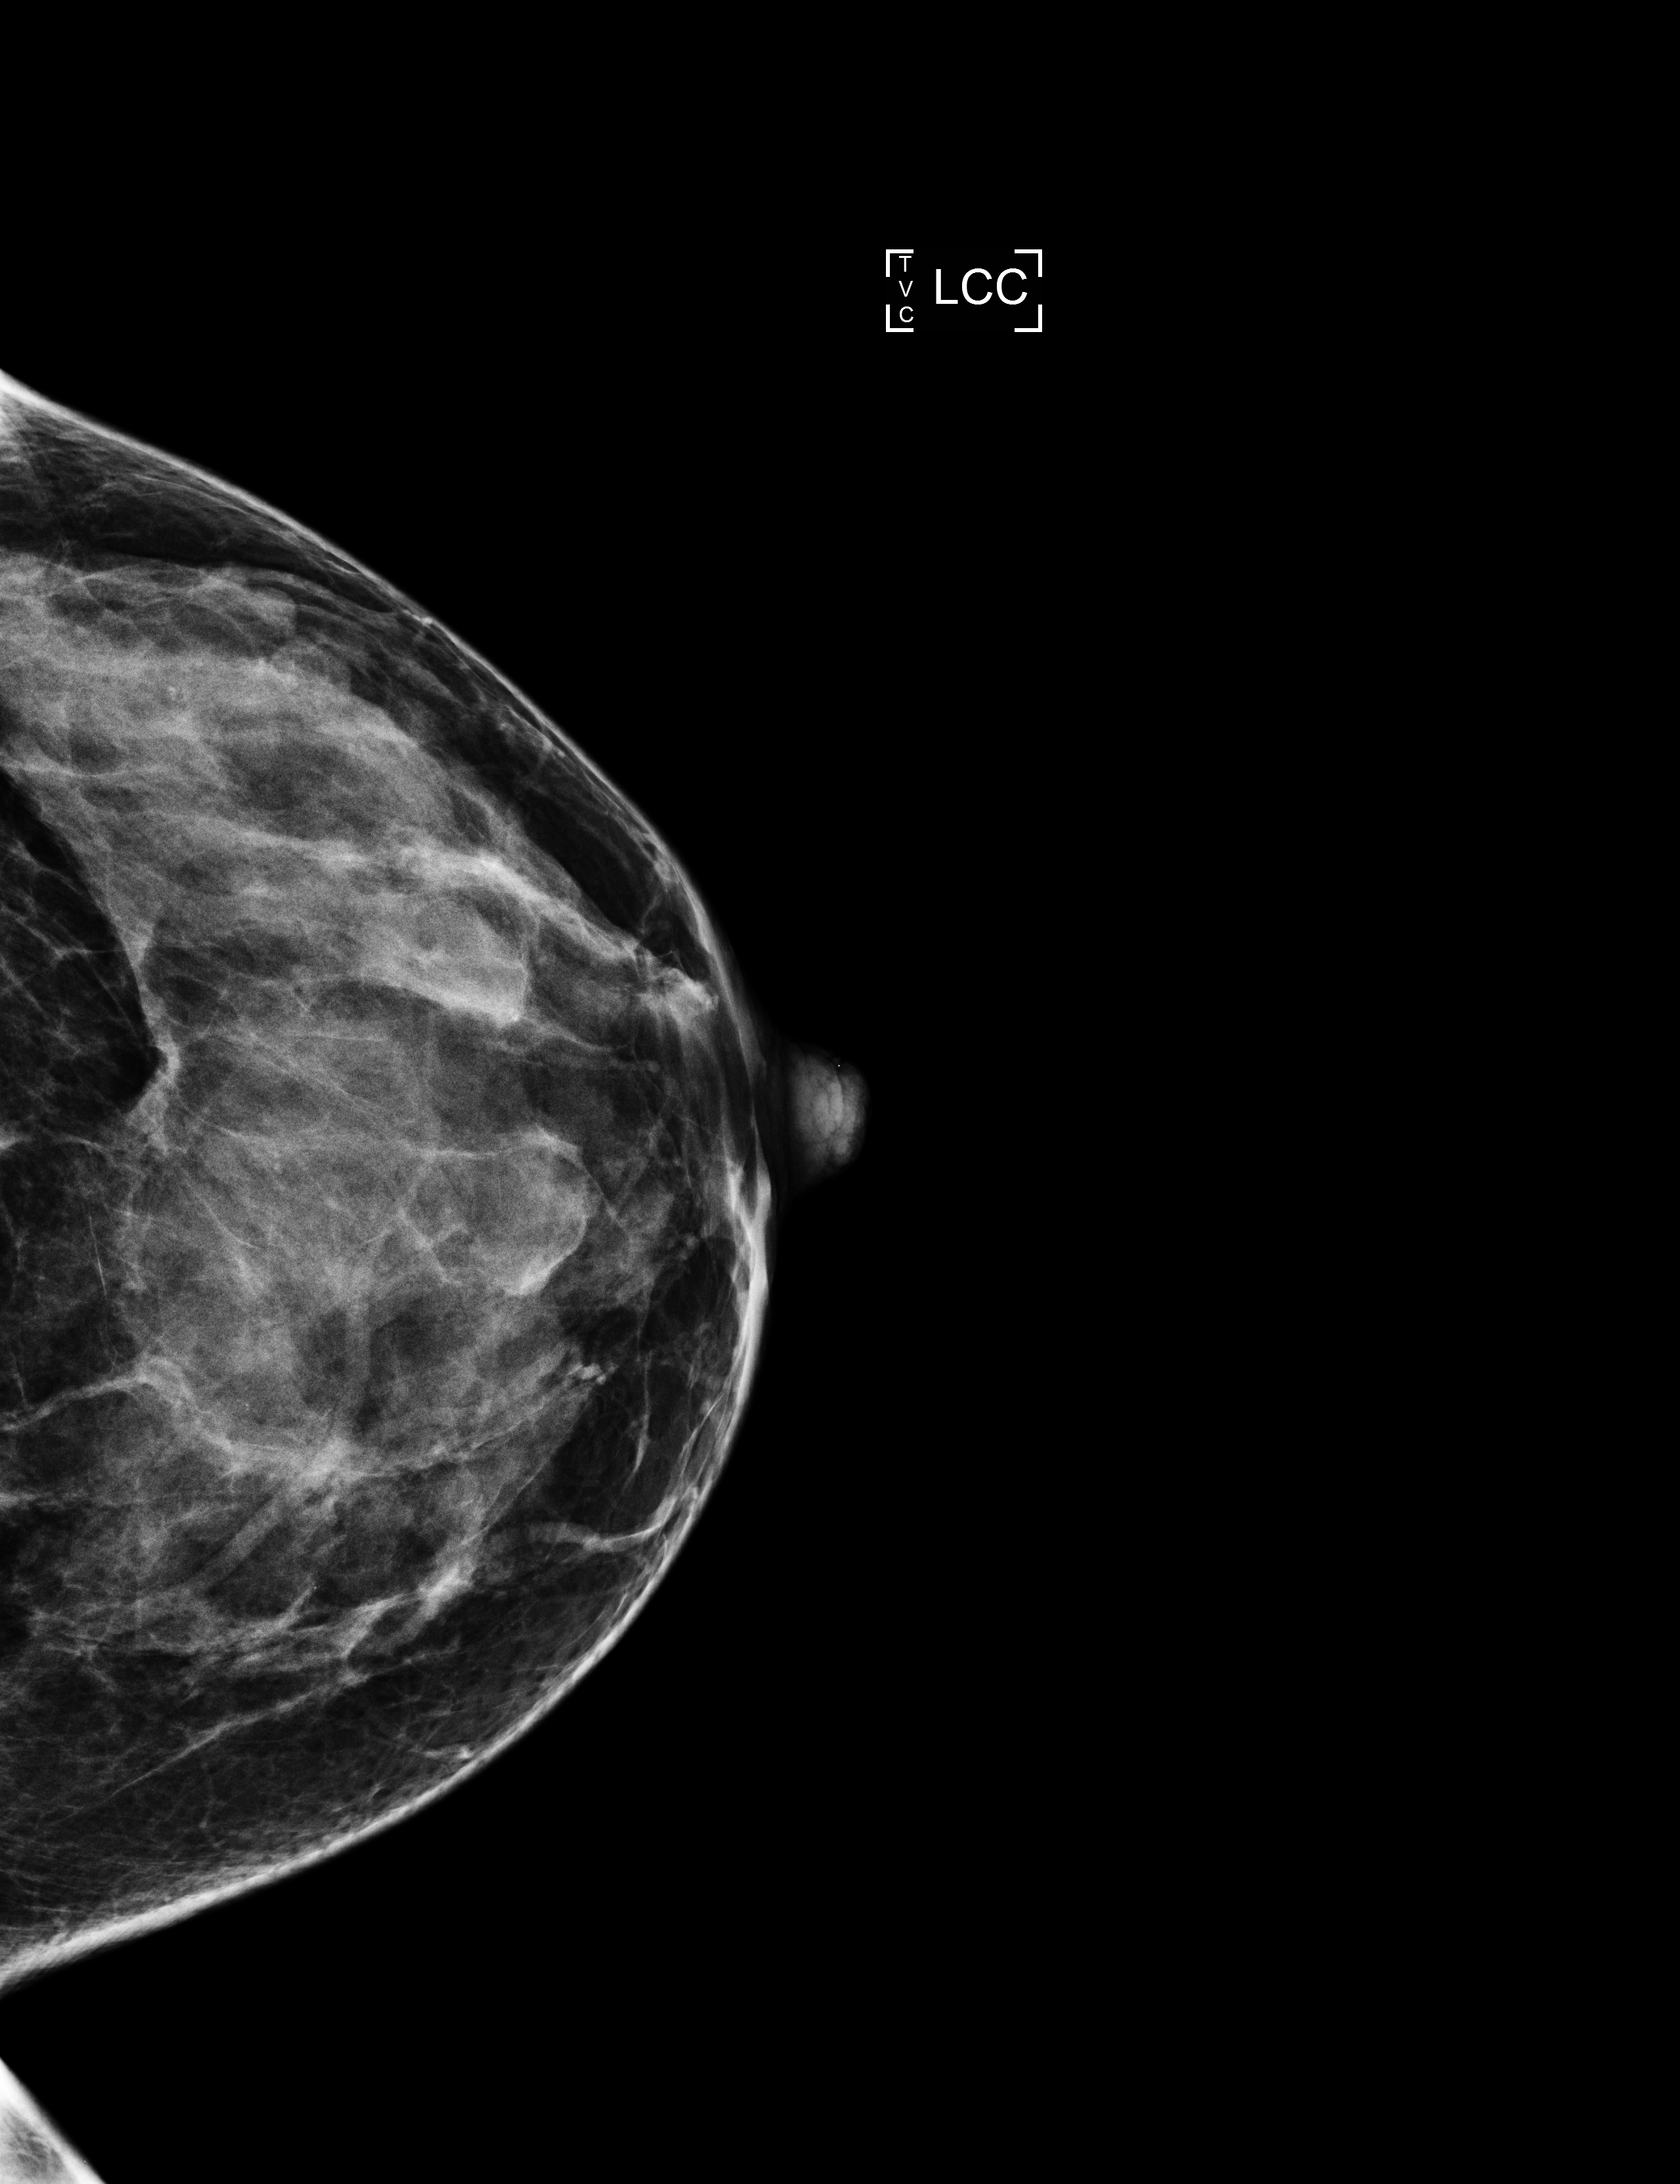
Screening examination. Female patient, age 50 years.
Image type: full-field digital mammogram. Breast: left. Projection: CC view.